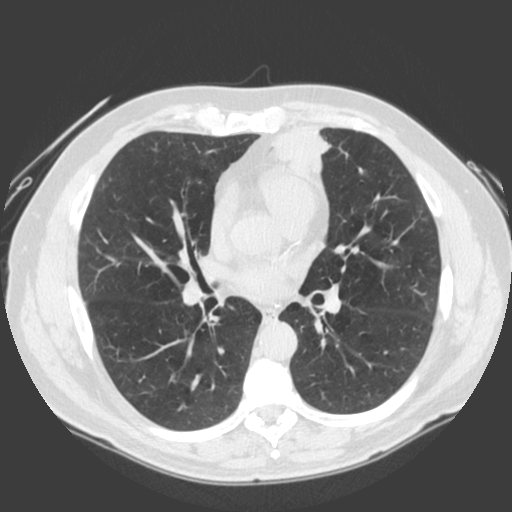
Low-dose screening chest CT, one axial slice. Slice 97 of 185 in the series (ordered by position). 120 kVp. Lung window (W 1500 / L -600 HU). 512 × 512 image matrix.
Structures marked on this image (expert manual segmentation):
- lesion 1 (tumor, lower lobe of left lung): box from (x=277, y=126) to (x=332, y=173) px